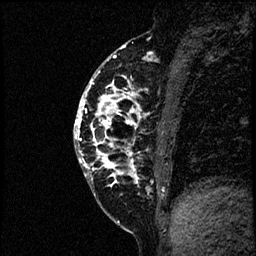
Breast MRI (dynamic contrast-enhanced), one sagittal slice; slice 25 of 60 in the series (ordered by position); dynamic contrast-enhanced study with each time point stored as its own series, time point 2 of 4 at this slice position (early post-contrast, ordered by acquisition time); 1.5 T; TE 4.2 ms, TR 17.6 ms; 2 mm slice thickness; 256 × 256 image matrix. Patient: female, 40 years. Case-level facts recorded for this patient, not image findings: setting: breast cancer imaged before/during neoadjuvant chemotherapy; receptor status: HER2-positive.
Annotated regions visible in this slice (semi-automatic segmentation, software-assisted and operator-edited):
- analysis volume of interest (the breast-tissue region the enhancement analysis was run in; not a lesion): bounding box [x1, y1, x2, y2] px = [75, 56, 197, 205]
- tumour enhancement mask (voxels above the 100 % enhancement threshold inside the analysis volume of interest): [75, 56, 153, 190]